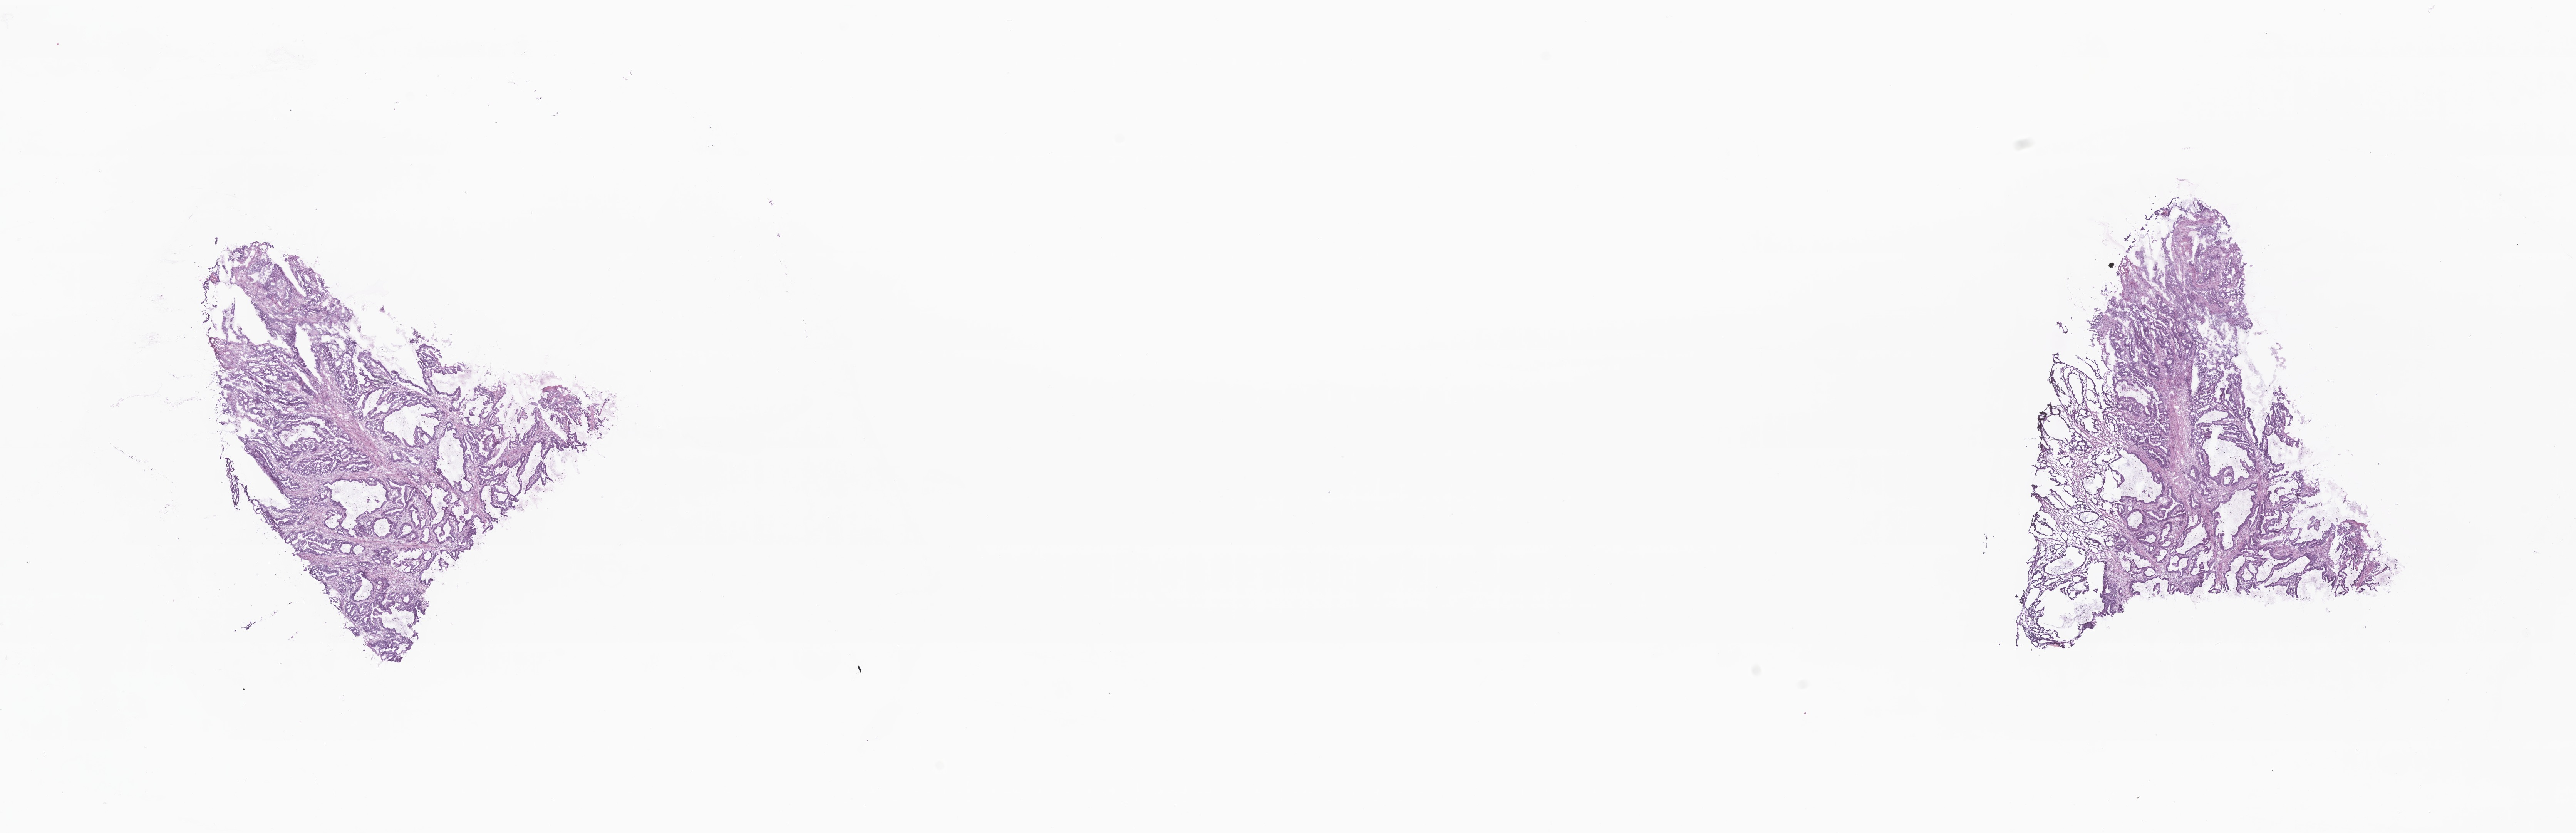
Digitized hematoxylin and eosin (H&E)-stained section — shown as a low-resolution overview of the whole scanned area (about 28.2 x 9.1 mm). Frozen section. Specimen: primary tumor. Site: ascending colon. Female patient; age at initial diagnosis 73 years. Slide review estimates, as recorded: tumor cells 100%, tumor nuclei 75%, stromal cells 0%, necrosis 0%, normal cells 0%. Inflammatory infiltration, as recorded: lymphocyte infiltration 0%, monocyte infiltration 0%, neutrophil infiltration 0%.
Diagnosis: Mucinous adenocarcinoma.